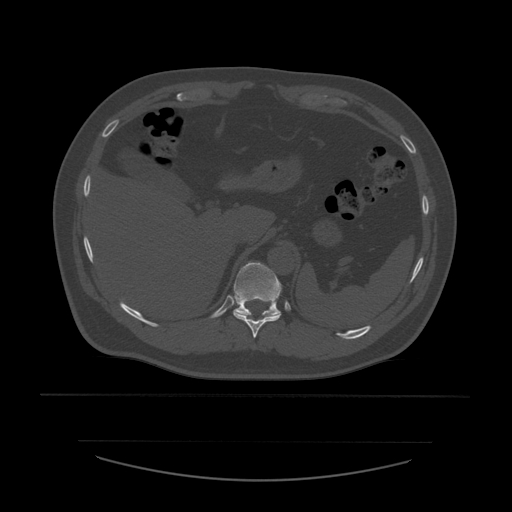
CT including the spine, one axial slice. Slice 287 of 532 in the series (ordered by position). Reconstruction kernel STANDARD. 120 kVp. Bone window (W 1800 / L 400 HU). 1.25 mm slice thickness. 512 × 512 image matrix. Patient age 44 years. From the clinical record (not read from this slice): primary cancer: soft tissue sarcoma.
Annotated regions visible in this slice (semi-automatic segmentation, software-assisted and operator-edited):
- T10 vertebra: bounding box [x1, y1, x2, y2] px = [233, 311, 281, 338]
- T11 vertebra: [234, 262, 282, 317]